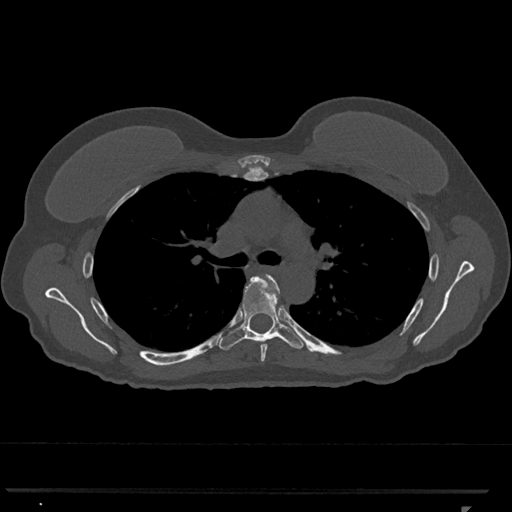
CT including the spine, one axial slice. Position 776 of 793 along the scan axis. 120 kVp. Bone window (W 1800 / L 400 HU). 0.5 mm slice thickness. 512 × 512 image matrix. Patient: female, 62 years. From the clinical record (not read from this slice): primary cancer: renal.
Outlined on this slice (semi-automatically segmented with operator editing):
- T5 vertebra: box from (x=260, y=274) to (x=280, y=362) px
- T6 vertebra: (x=219, y=275)–(x=304, y=350)